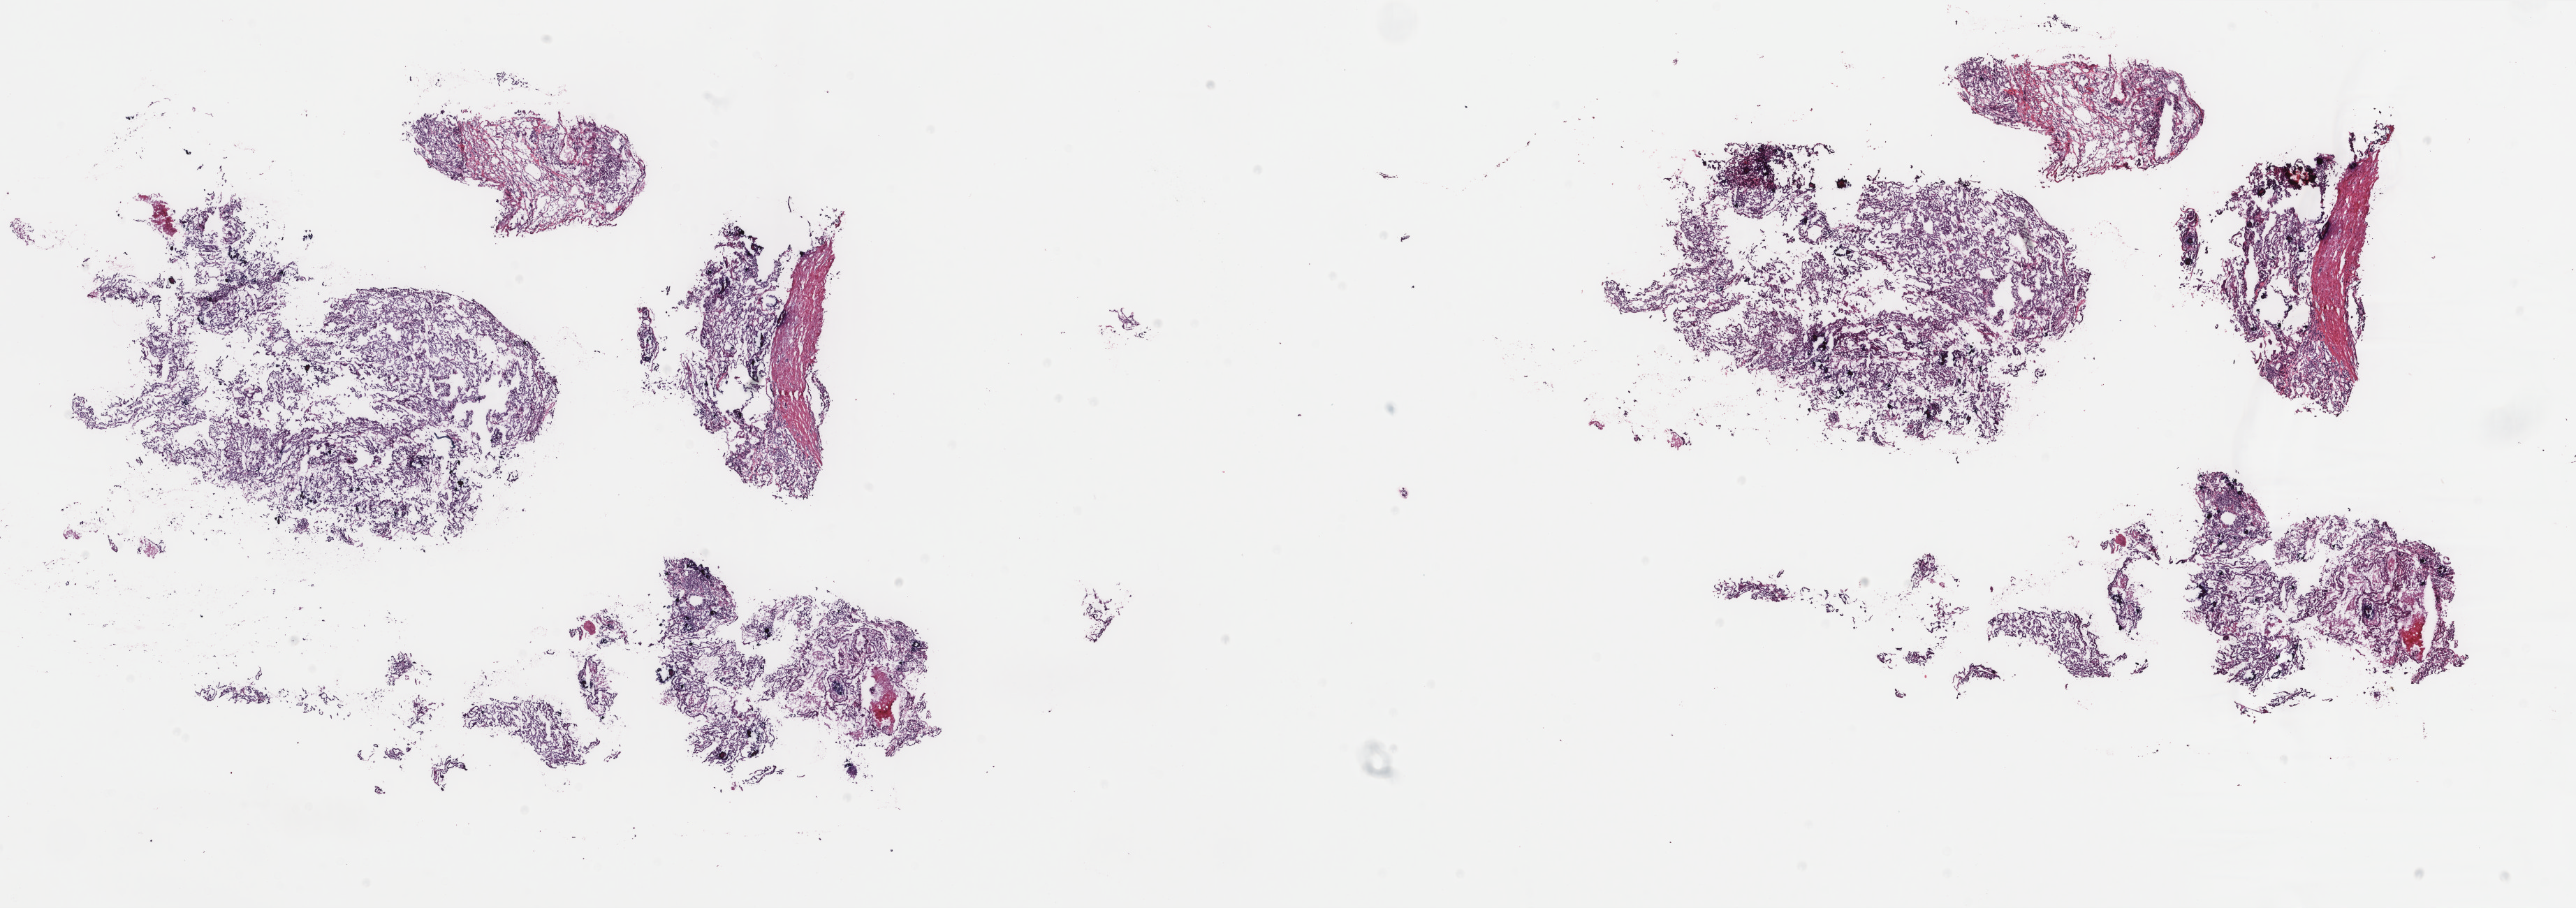
Hematoxylin and eosin (H&E) stained whole-slide image — whole scanned area (about 29.3 x 10.3 mm, slide scanned at 40x) shown as a low-resolution overview. Frozen section from the top of the tissue portion. Thyroid, primary tumour sample. Patient: female, age at initial diagnosis 30 years. Composition of this section per pathologist review: tumour cells 80%, tumour nuclei 80%, normal cells 0%, stromal cells 20%, necrosis 0%. Inflammatory infiltration, as recorded: lymphocyte infiltration 5%, monocyte infiltration 0%, neutrophil infiltration 0%.
* AJCC pathologic stage: I (7th edition)
* lymph nodes positive (case pathology): 0 of 2 examined
* histologic diagnosis: Papillary adenocarcinoma, NOS (thyroid gland)